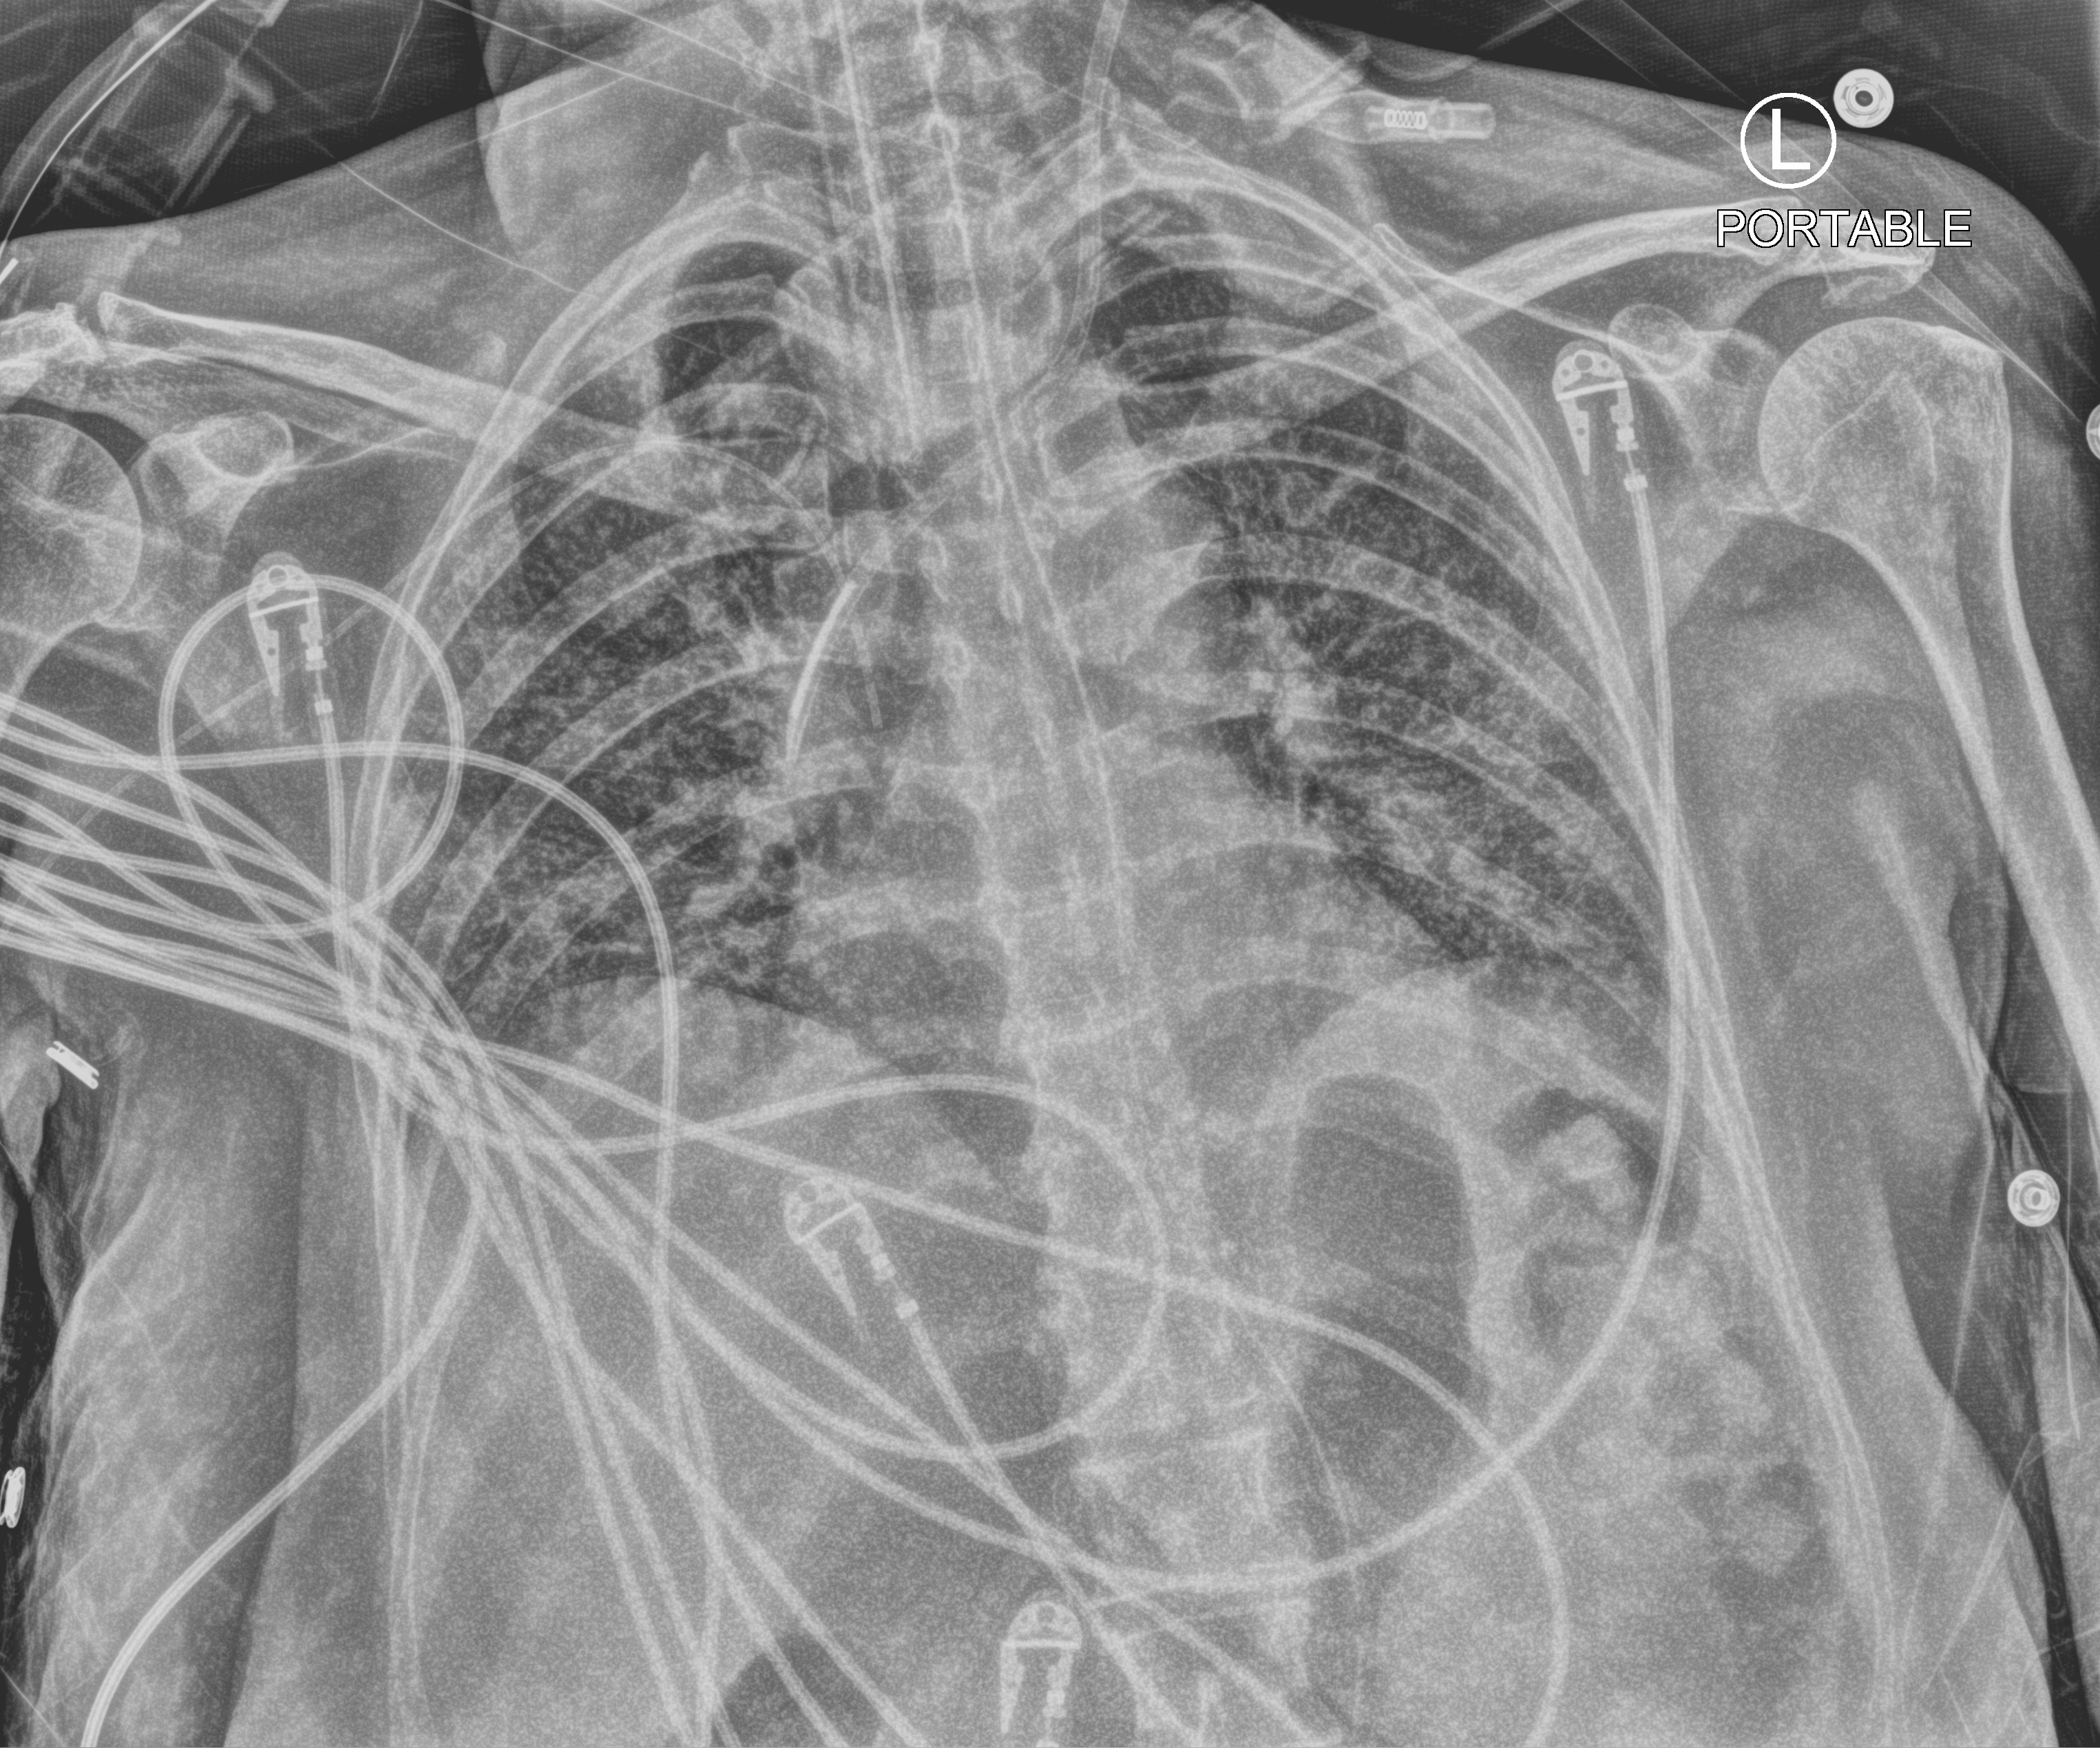
Chest X-ray (portable); anteroposterior (AP) projection. Patient hospitalised with COVID-19; female, aged 60–74 years.
Admission-level facts for this patient (not findings on this image; timing relative to this image not recorded): admitted to intensive care during this hospital stay: yes; COPD (admission record): no.